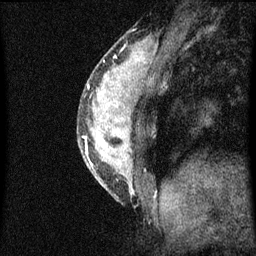
Breast MRI (dynamic contrast-enhanced), one sagittal slice. Position 21 of 60 along the scan axis. Dynamic contrast-enhanced series, image 2 of 3 at this slice position (ordered by acquisition). 1.5 T. TE 4.2 ms, TR 8 ms. 2 mm slice thickness. 256 × 256 image matrix, field of view 180 × 180 mm. Female patient, age 33 years.
Annotated regions visible in this slice (semi-automatic segmentation, software-assisted and operator-edited):
- analysis volume of interest (the breast-tissue region the enhancement analysis was run in; not a lesion): bounding box <78,56,152,201> (left, top, right, bottom; pixels)
- tumour enhancement mask (voxels above the 70 % enhancement threshold inside the analysis volume of interest): <83,62,134,193>